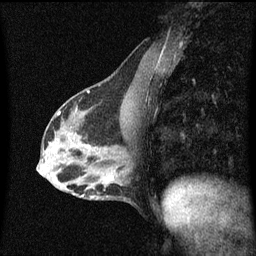
Breast MRI (dynamic contrast-enhanced), one sagittal slice; position 28 of 60 along the scan axis; dynamic contrast-enhanced series, image 2 of 3 at this slice position (ordered by acquisition); 1.5 T; TE 4.2 ms, TR 8.4 ms; 2 mm slice thickness; 256 × 256 image matrix. Female patient, age 40 years.
Annotated regions visible in this slice (semi-automatically segmented with operator editing):
- analysis volume of interest (the breast-tissue region the enhancement analysis was run in; not a lesion): bounding box [x1, y1, x2, y2] px = [78, 166, 120, 201]
- tumour enhancement mask (voxels above the 70 % enhancement threshold inside the analysis volume of interest): [83, 176, 114, 199]